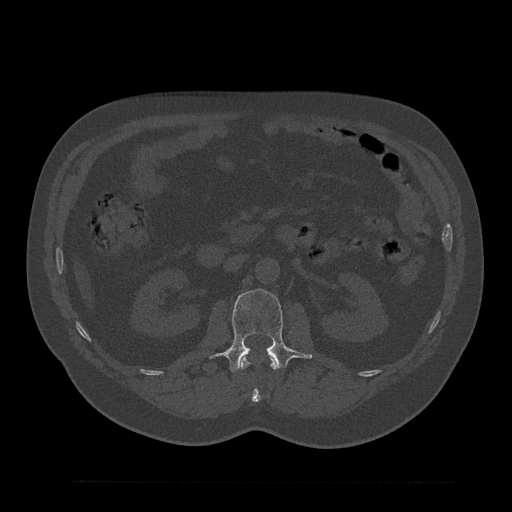
CT including the spine, one axial slice; reconstruction kernel Br40s/3; bone window (W 1800 / L 400 HU); 0.5 mm slice thickness; 512 × 512 image matrix. Male patient, age 61 years. Case-level facts recorded for this patient, not image findings: primary cancer: prostate.
Annotated regions visible in this slice (semi-automatically segmented with operator editing):
- L1 vertebra: box from (x=241, y=353) to (x=277, y=403) px
- L2 vertebra: (x=211, y=289)–(x=312, y=372)